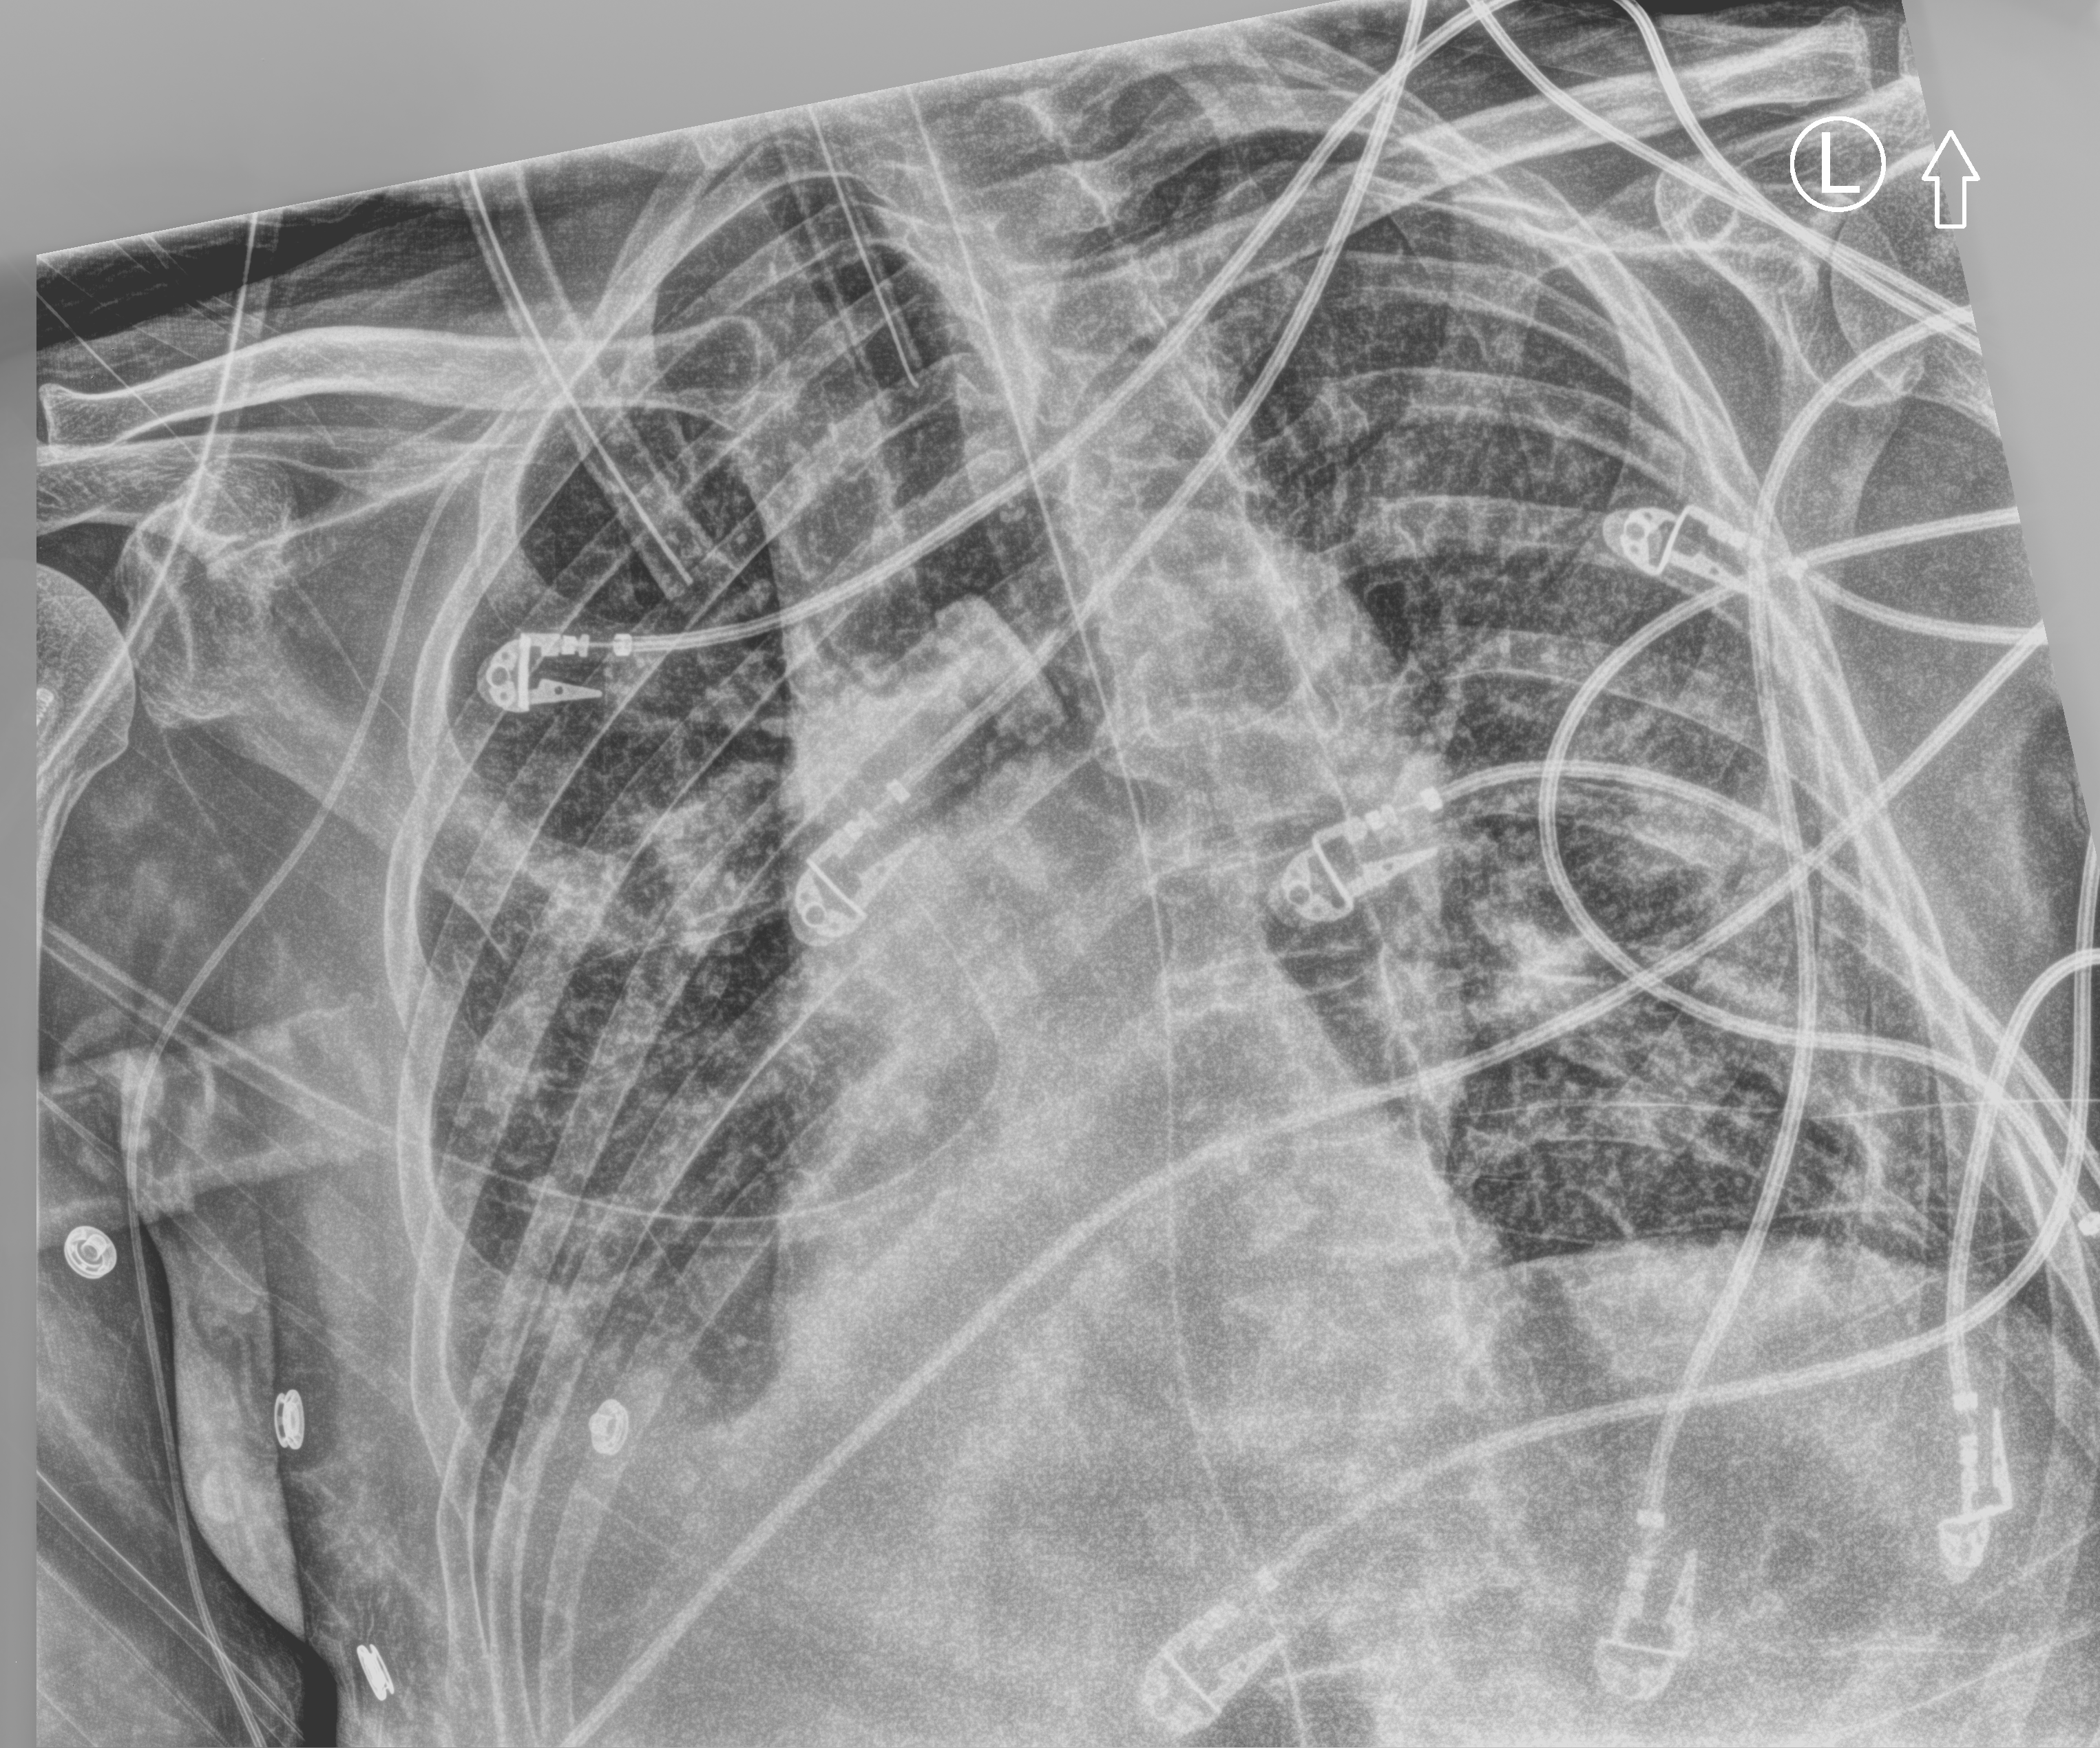
Bedside chest radiograph (computed radiography). Male patient hospitalised with COVID-19, age 75–90 years.
Admission-level facts for this patient (not findings on this image; timing relative to this image not recorded): length of hospital stay: 70 days; admitted to intensive care during this hospital stay: yes.